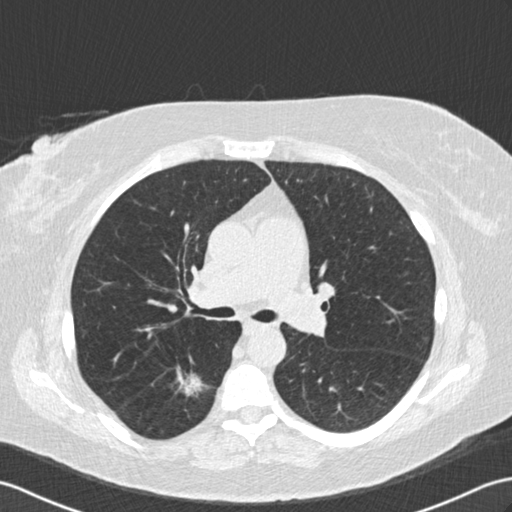
Chest CT (low-dose screening protocol), one axial image; second annual screen; lung window (W 1500 / L -600 HU); standard (soft-tissue) reconstruction kernel (B30f); slice 59 of 154 in the series. Female, age 65 years at enrolment. Former smoker at enrolment.
Lesion marked by an expert reader, box from (x=157, y=356) to (x=214, y=413) px. Reader record for this screening exam (exam-level; its link to the box is not recorded): non-calcified nodule or mass ≥4 mm, right lower lobe, 18 × 16 mm, spiculated (stellate) margins, soft tissue attenuation, pre-existing on the prior screen: yes; interval growth: yes. Official screen result: positive, other. Lung cancer was diagnosed 239 days after this screen: adenocarcinoma, NOS, right lower lobe, moderately differentiated (G2), stage IA (AJCC 6th edition), 25 mm at pathology.